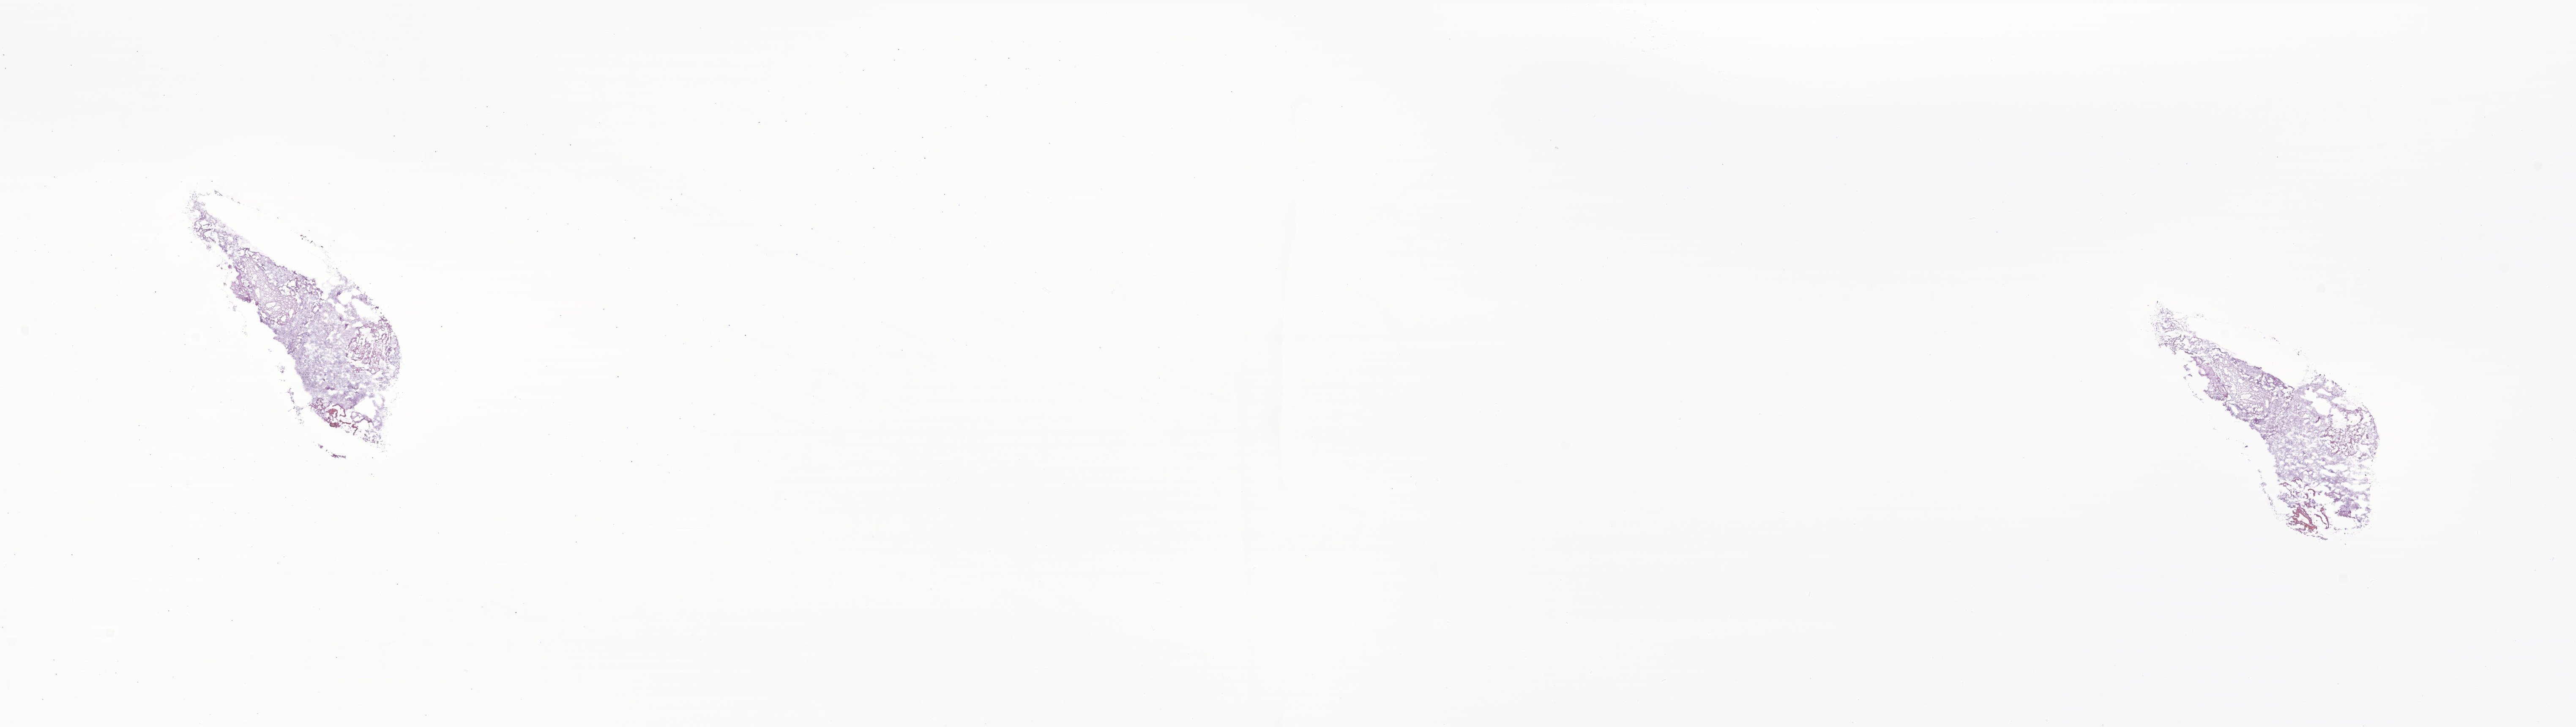
Whole-slide image, haematoxylin and eosin stain of tumor tissue from the brain, a low-resolution overview of the entire scanned area, about 25.7 x 7.3 mm, frozen section. Patient female; age 42 months (3 years 6 months).
Recorded diagnosis: Pilocytic astrocytoma.